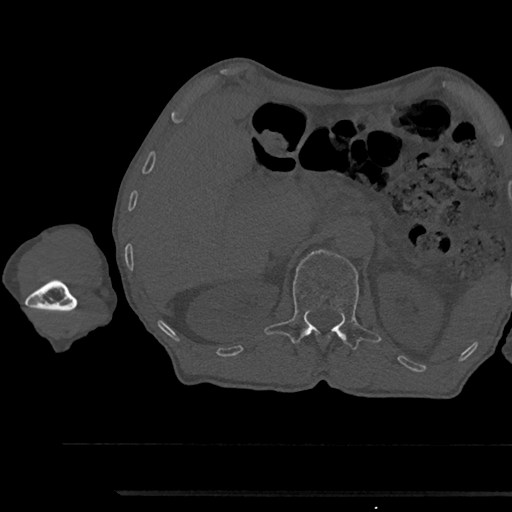
CT including the spine, one axial slice; position 651 of 797 along the scan axis; reconstruction kernel Br40s/3; bone window (W 1800 / L 400 HU); 0.5 mm slice thickness; 512 × 512 image matrix, field of view 367 × 367 mm. Male patient, age 79 years. From the clinical record (not read from this slice): primary cancer: prostate.
Annotated regions visible in this slice (semi-automatic segmentation, software-assisted and operator-edited):
- L1 vertebra: bounding box <264,249,381,350> (left, top, right, bottom; pixels)